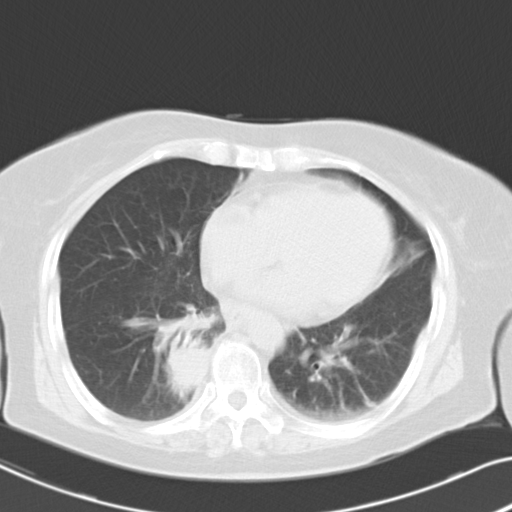
Chest CT, one axial slice; position 10 of 26 along the scan axis; reconstruction kernel B40f; lung window (W 1500 / L -600 HU); 10 mm slice thickness; 512 × 512 image matrix, field of view 333 × 333 mm. Female patient, age 70 years. Case-level facts recorded for this patient, not image findings: clinical TNM (as recorded): T2 N1 M1a.
Annotated regions visible in this slice (bounding box drawn by a radiologist):
- lung tumour (recorded histology: adenocarcinoma): bounding box <162,338,213,395> (left, top, right, bottom; pixels)